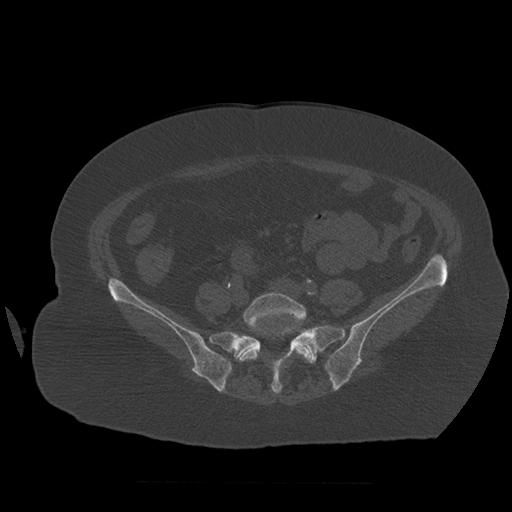
CT including the spine, one axial slice. Slice 173 of 399 in the series (ordered by position). Reconstruction kernel STANDARD. 120 kVp. Bone window (W 1800 / L 400 HU). 1.25 mm slice thickness. 512 × 512 image matrix, field of view 404 × 404 mm. Patient age 81 years. Case-level facts recorded for this patient, not image findings: primary cancer: renal; vertebrae with lytic lesions (as recorded): L1.
Outlined on this slice (semi-automatic segmentation, software-assisted and operator-edited):
- L5 vertebra: bounding box (x1, y1, x2, y2) in pixels: (237, 293, 313, 362)